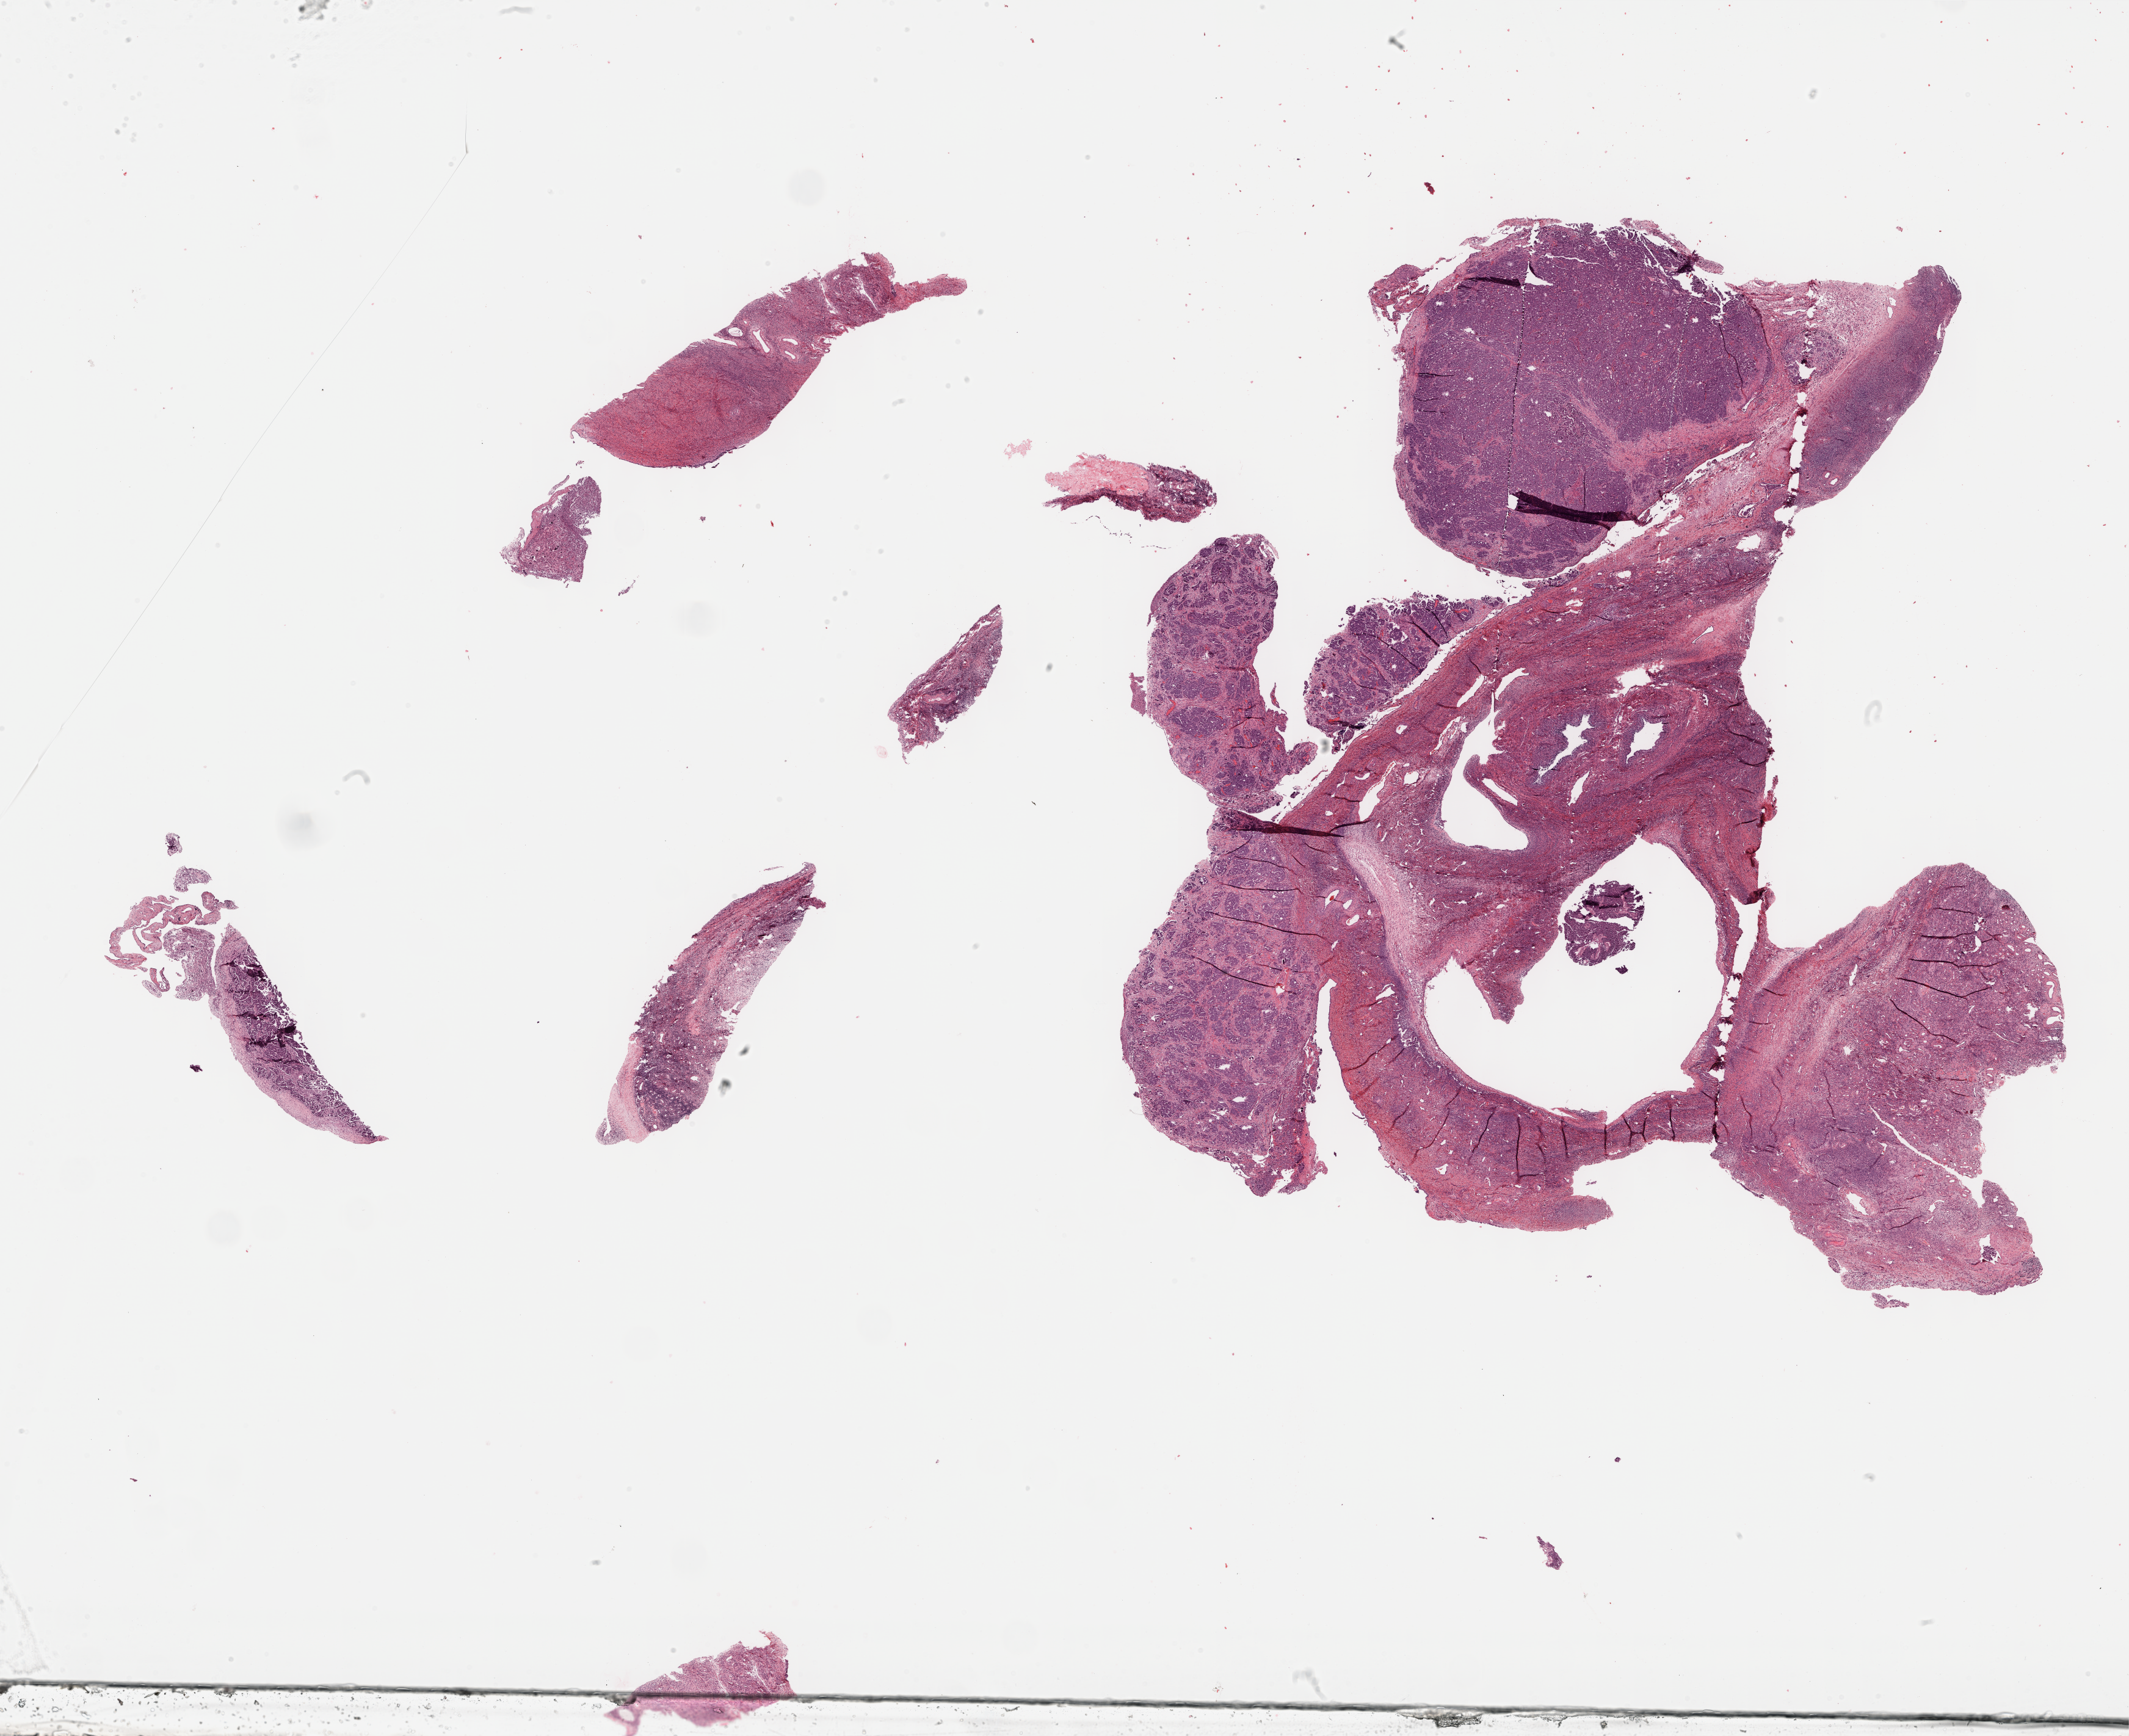
Whole-slide histology image, Hematoxylin and eosin (H&E) stained, shown as a low-resolution overview of the whole scanned area (about 28.2 x 23.0 mm), formalin-fixed paraffin-embedded (FFPE) diagnostic section, sample: primary tumour, ovary. Patient: female, age at initial diagnosis 38 years. Histologic grade: G3 (poorly differentiated).
• pathologic diagnosis: Serous cystadenocarcinoma, NOS
• laterality: bilateral
• FIGO stage: IIIC